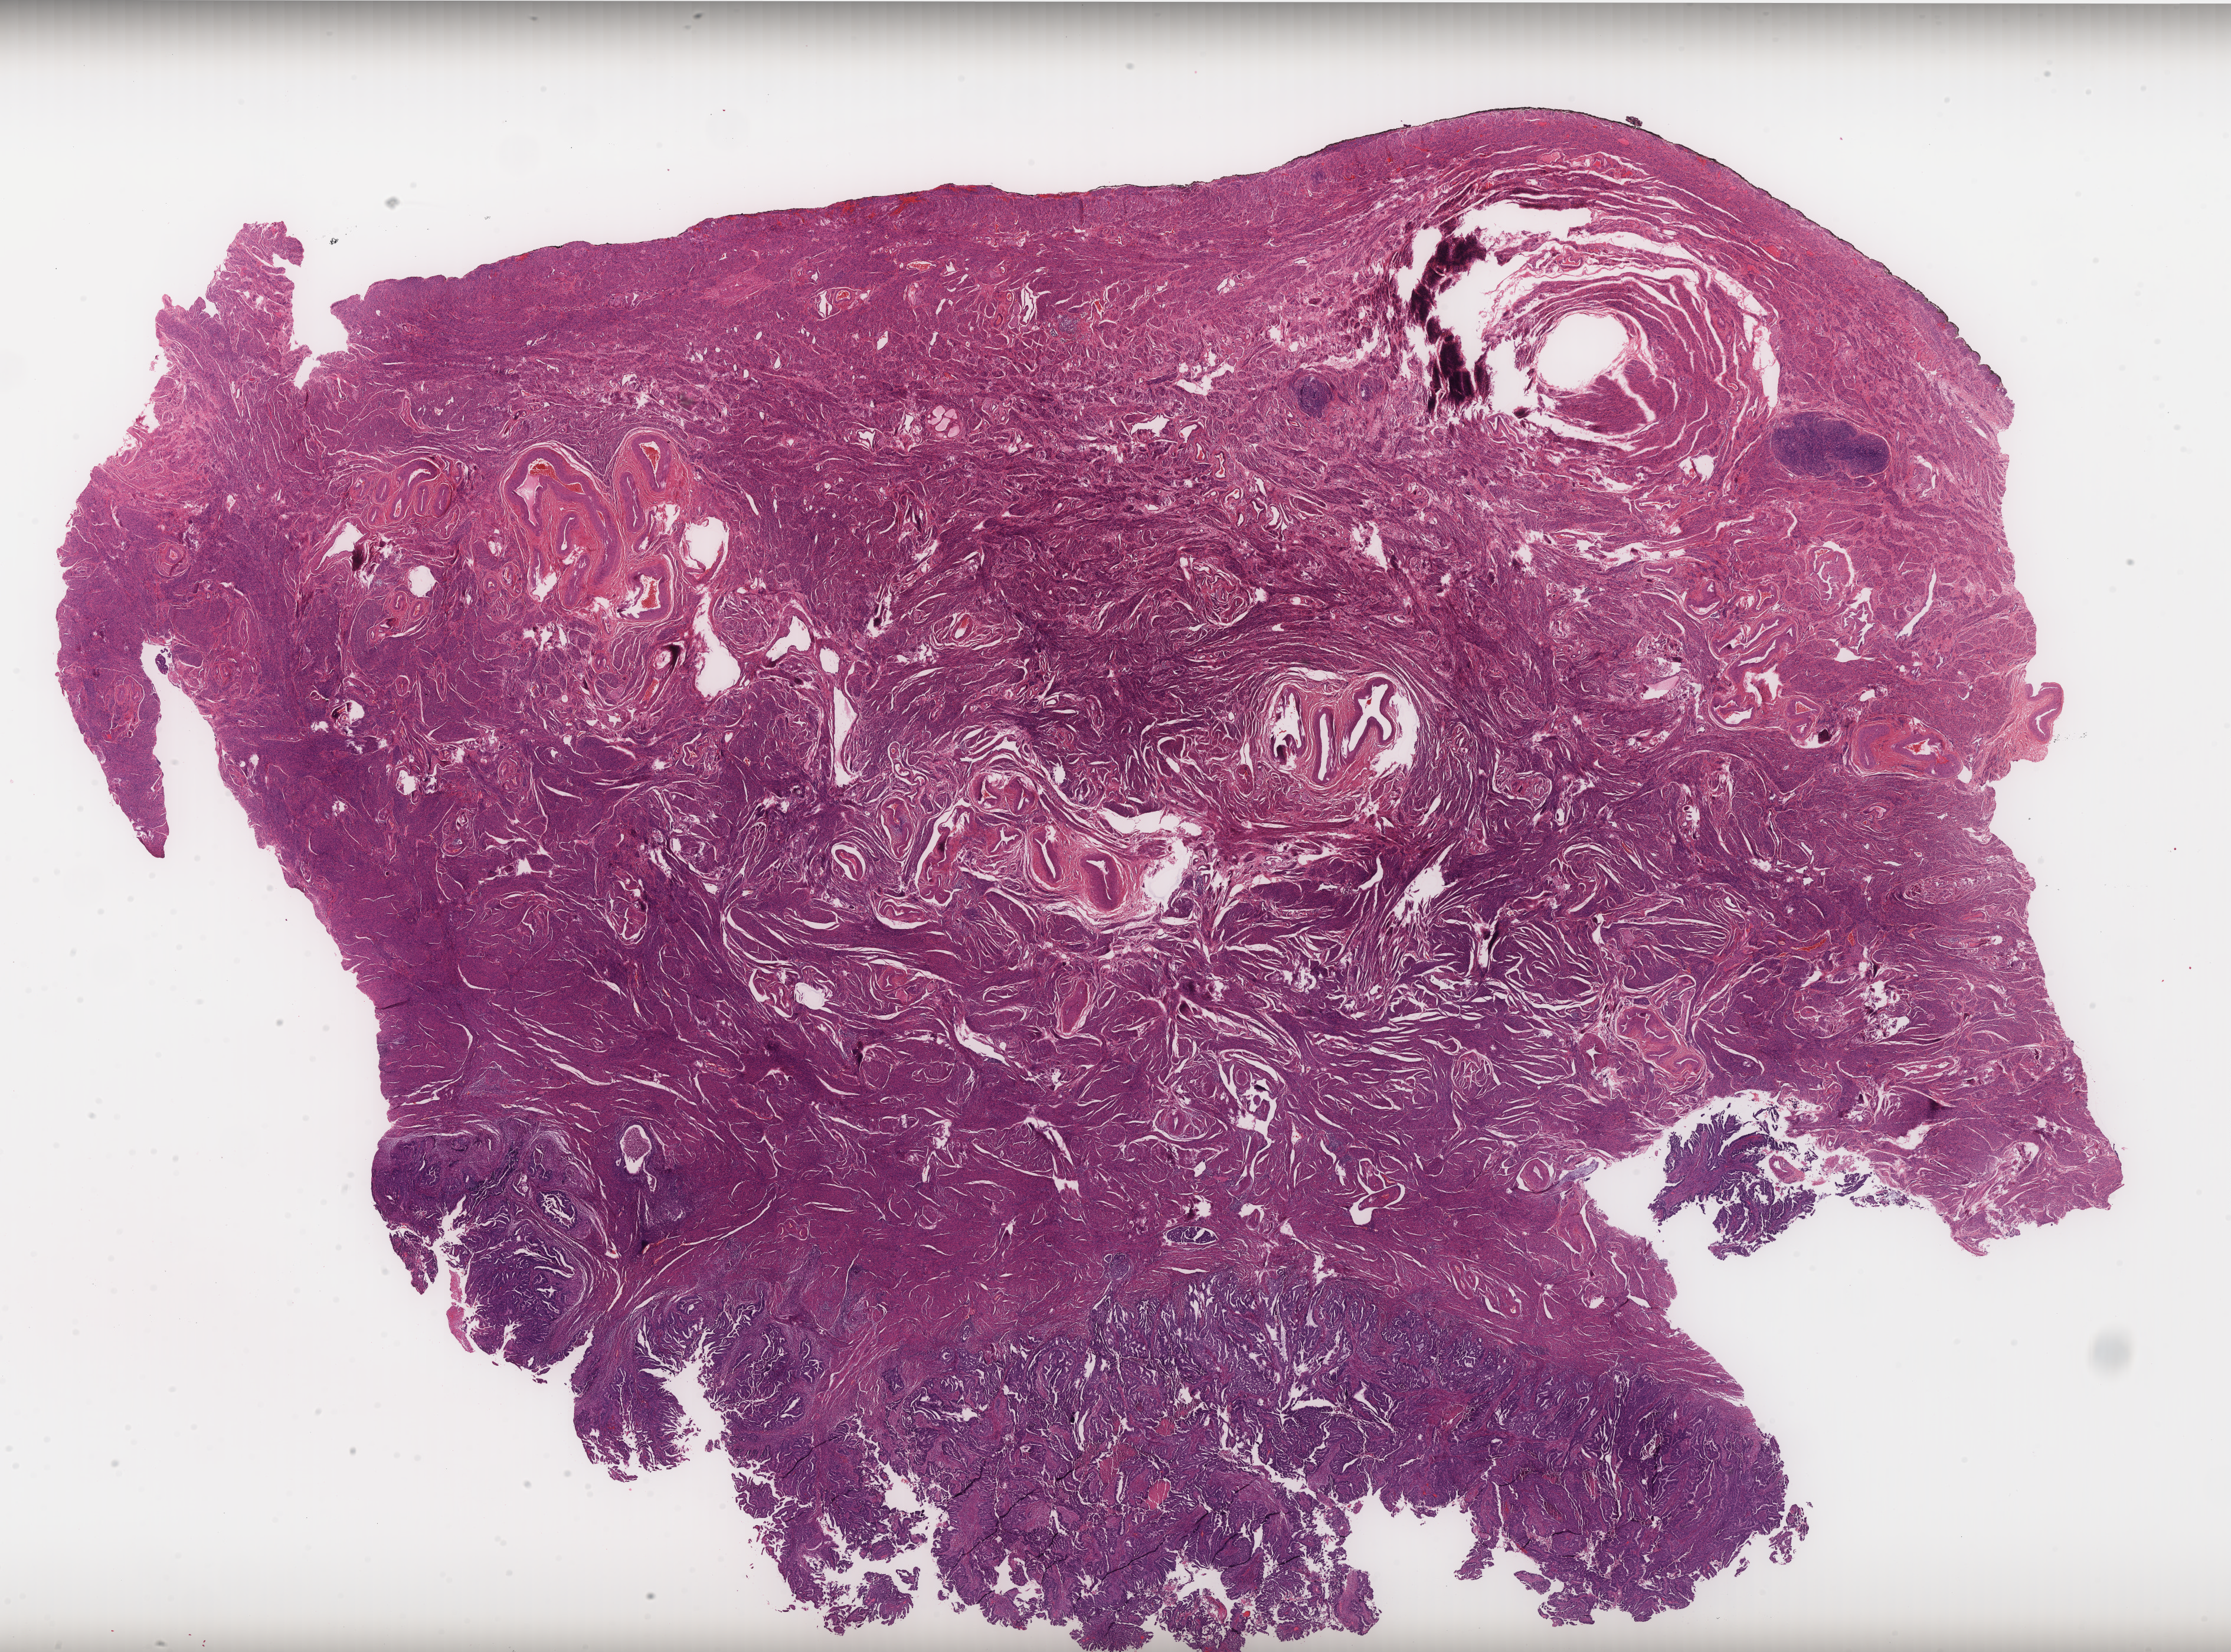
Hematoxylin and eosin (H&E) stained whole-slide image, shown as a low-resolution overview of the whole scanned area (about 30.3 x 22.4 mm, from a 40x scan). Formalin-fixed paraffin-embedded (FFPE) diagnostic section. Sample: primary tumour, uterus. Patient: female, age at initial diagnosis 57 years.
Pathologic diagnosis: Endometrioid adenocarcinoma, NOS (endometrium).